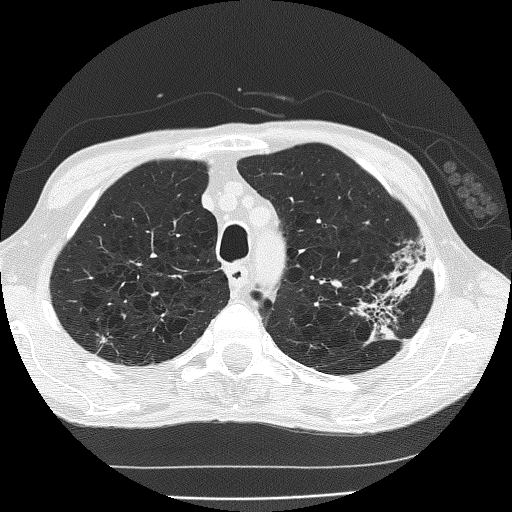
Low-dose screening chest CT, one axial slice; position 146 of 185 along the scan axis; reconstruction kernel FC51; 120 kVp; lung window (W 1500 / L -600 HU); 2 mm slice thickness; 512 × 512 image matrix.
Outlined on this slice (outlined manually by an expert reader):
- lesion 1 (tumor, upper lobe of left lung): bounding box <382,257,424,299> (left, top, right, bottom; pixels)